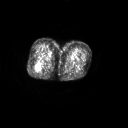
FDG PET of an extremity soft-tissue mass (from a PET/CT study), one axial slice. Slice 25 of 267 in the series (ordered by position). 3.27 mm slice thickness. 128 × 128 image matrix, field of view 700 × 700 mm. Female patient, age 70 years. Case-level facts recorded for this patient, not image findings: histological type: synovial sarcoma; grade: intermediate; site of the primary tumour: right buttock.
Structures marked on this image (expert contour drawn on MRI and transferred to this co-registered scan by the dataset authors):
- gross tumour volume including surrounding oedema: bounding box [x1, y1, x2, y2] px = [35, 61, 40, 70]